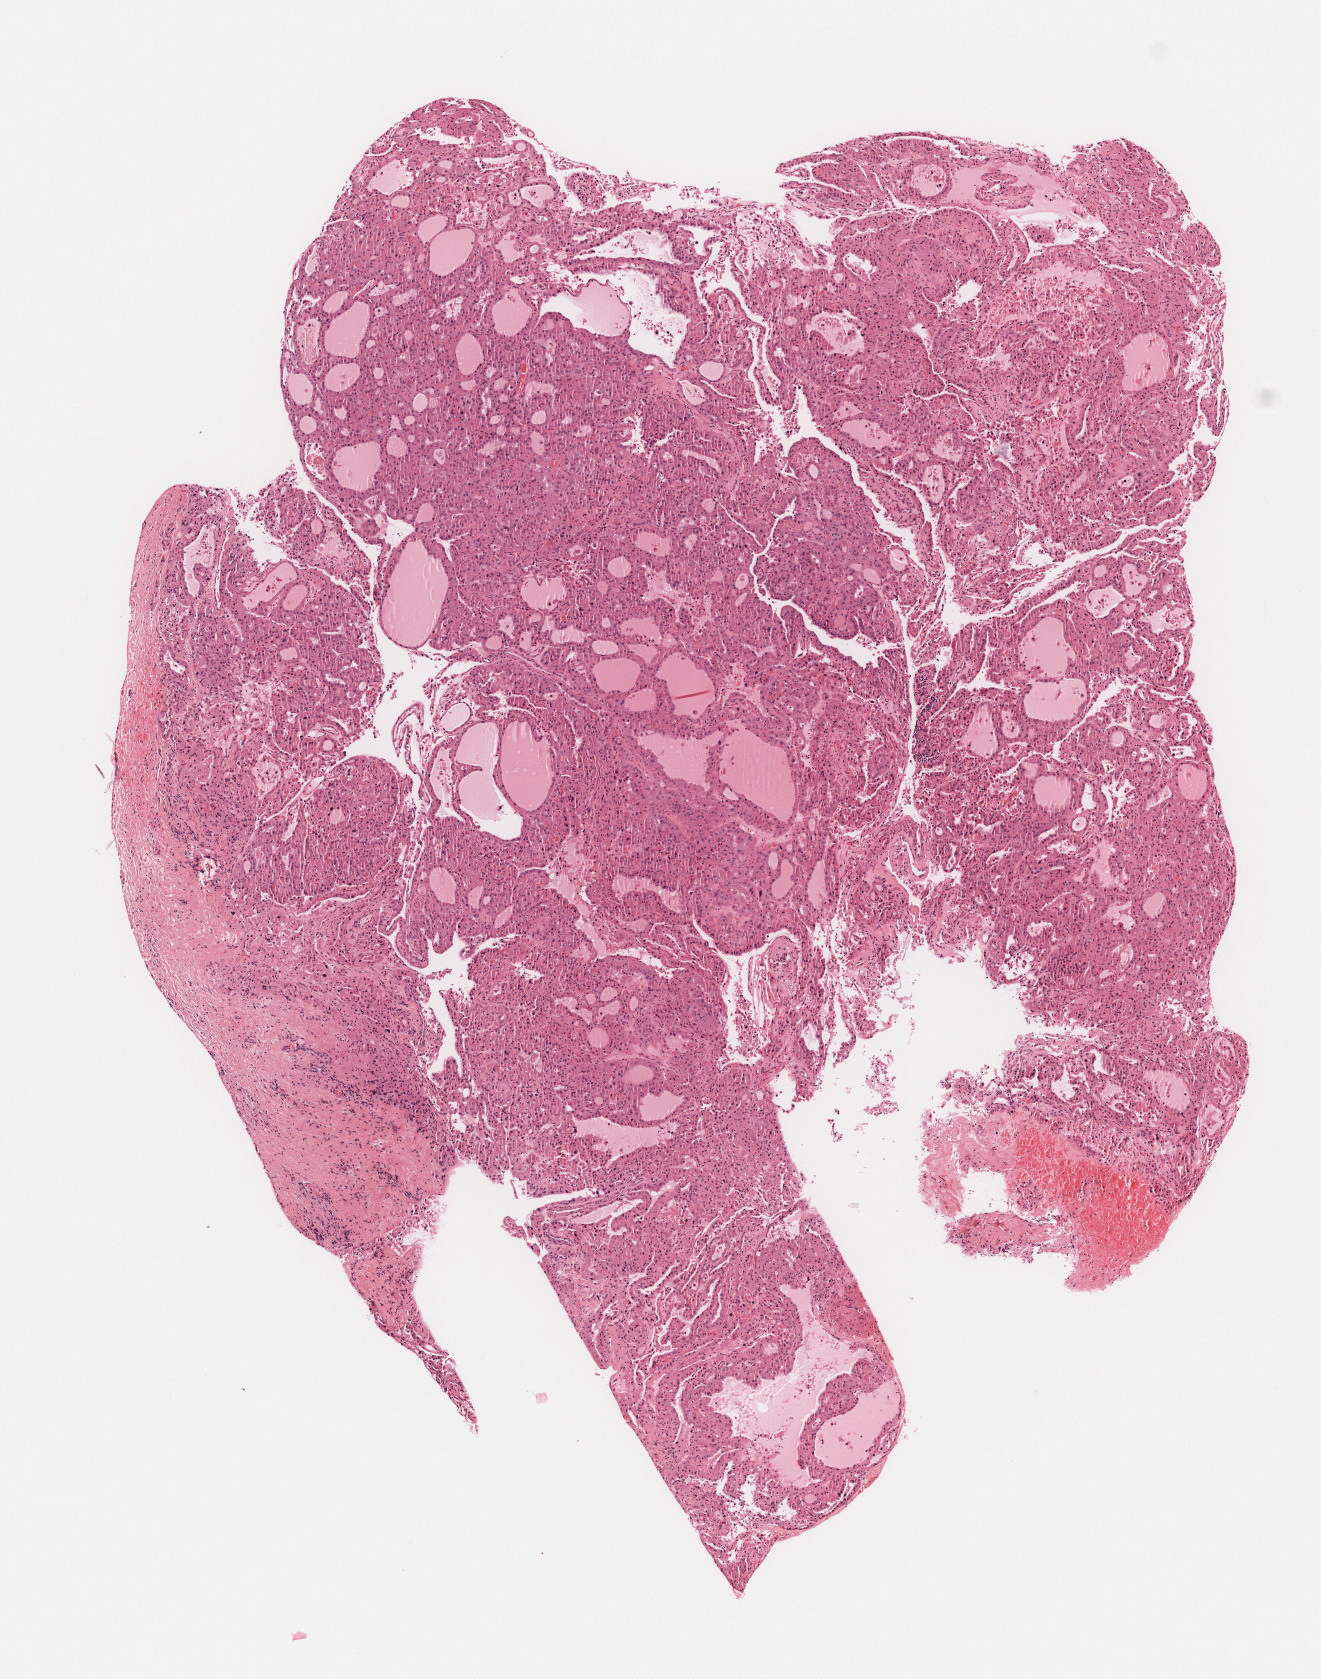
Hematoxylin and eosin (H&E) stained whole-slide image — shown as a low-resolution overview of the whole scanned area (about 5.3 x 6.8 mm, acquisition: 40x scan), formalin-fixed paraffin-embedded (FFPE) diagnostic section, thyroid, primary tumour sample. Female patient; age at initial diagnosis 37 years.
* TNM: T1b NX MX
* AJCC pathologic stage: I (7th edition)
* laterality: right
* diagnosis: Papillary carcinoma, follicular variant (thyroid gland)